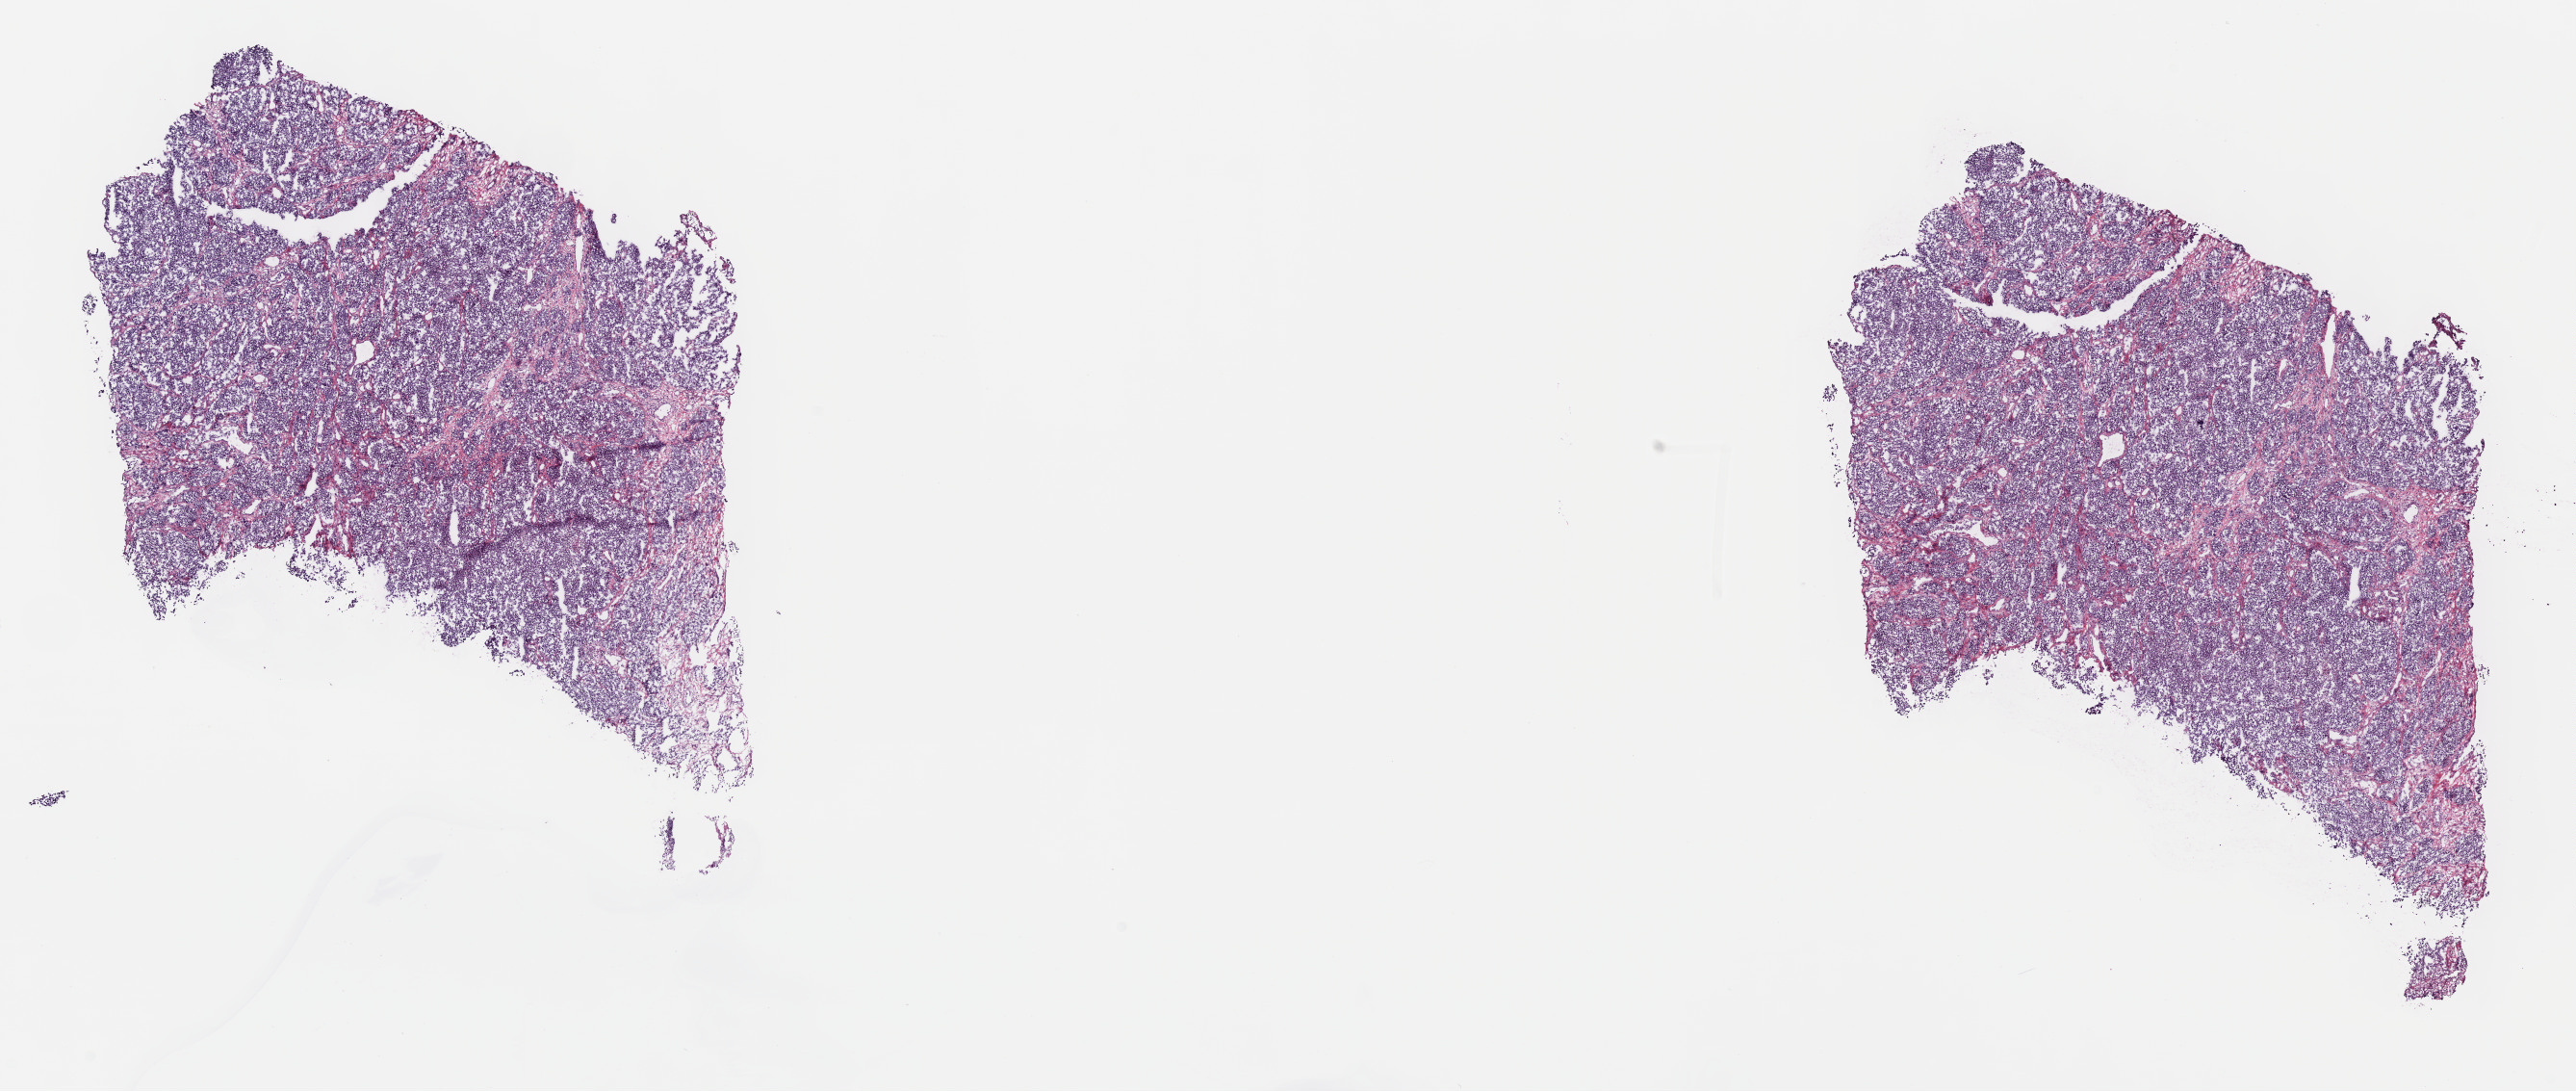
Whole-slide histology image, H&E — low-resolution overview of the scanned area, about 21.6 x 9.2 mm, frozen section from the top of the tissue portion, skin, primary tumour sample. Male, age 55 years at initial diagnosis. Slide review estimates, as recorded: tumour cells 100%, tumour nuclei 75%, normal cells 0%, stromal cells 0%, necrosis 0%. Inflammatory infiltration, as recorded: lymphocyte infiltration 2%, monocyte infiltration 0%, neutrophil infiltration 0%.
AJCC pathologic stage: III (7th edition). Diagnosis: Epithelioid cell melanoma.